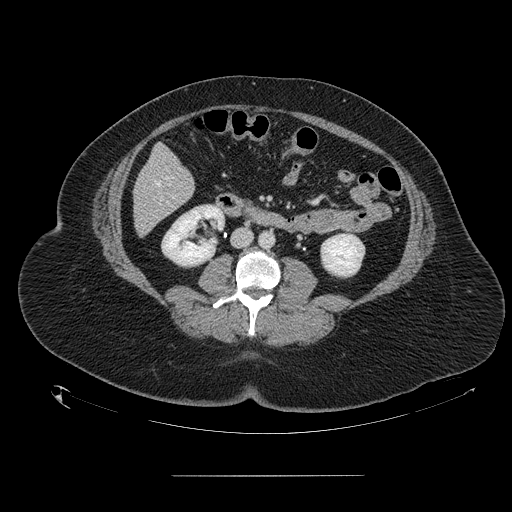
Contrast-enhanced abdominal CT, one axial slice. Position 39 of 164 along the scan axis. Intravenous contrast given. Soft-tissue window (W 400 / L 40 HU). 2.5 mm slice thickness. 512 × 512 image matrix, field of view 495 × 495 mm. Female patient, age 52 years. From the clinical record (not read from this slice): diagnosis: colorectal cancer liver metastases, imaged before liver resection; multiple liver metastases: yes.
Structures marked on this image (manually delineated by an expert):
- hepatic veins: bounding box [x1, y1, x2, y2] px = [155, 182, 160, 186]
- liver: [134, 146, 194, 235]